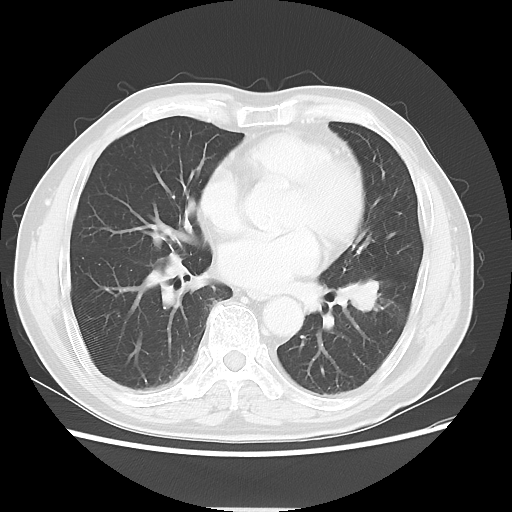
Chest CT, one axial slice. Lung window (W 1500 / L -600 HU). 5 mm slice thickness. 512 × 512 image matrix, field of view 366 × 366 mm. Patient: male, 71 years. Case-level facts recorded for this patient, not image findings: clinical TNM (as recorded): T1c N1 M0; histopathological grade: G2-3.
Annotated regions visible in this slice (rectangle marked by the reading radiologist):
- lung tumour (recorded histology: adenocarcinoma): bounding box (x1, y1, x2, y2) in pixels: (346, 270, 384, 319)